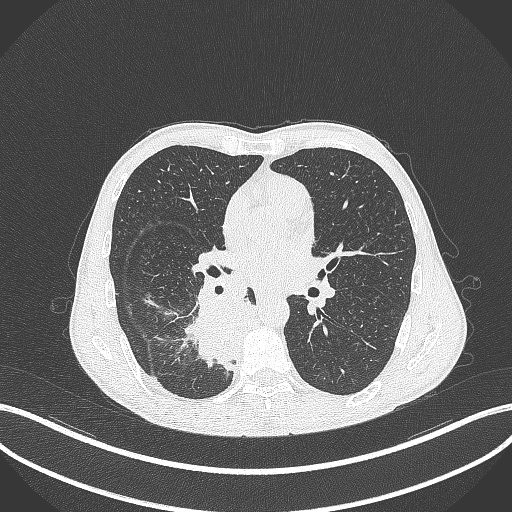
Chest CT, one axial slice; slice 192 of 371 in the series (ordered by position); lung window (W 1500 / L -600 HU); 1 mm slice thickness; 512 × 512 image matrix, field of view 400 × 400 mm. Male patient, age 58 years. From the clinical record (not read from this slice): clinical TNM (as recorded): T3 N1 M1.
Structures marked on this image (bounding box drawn by a radiologist):
- lung tumour (recorded histology: squamous cell carcinoma): bounding box <178,290,258,368> (left, top, right, bottom; pixels)